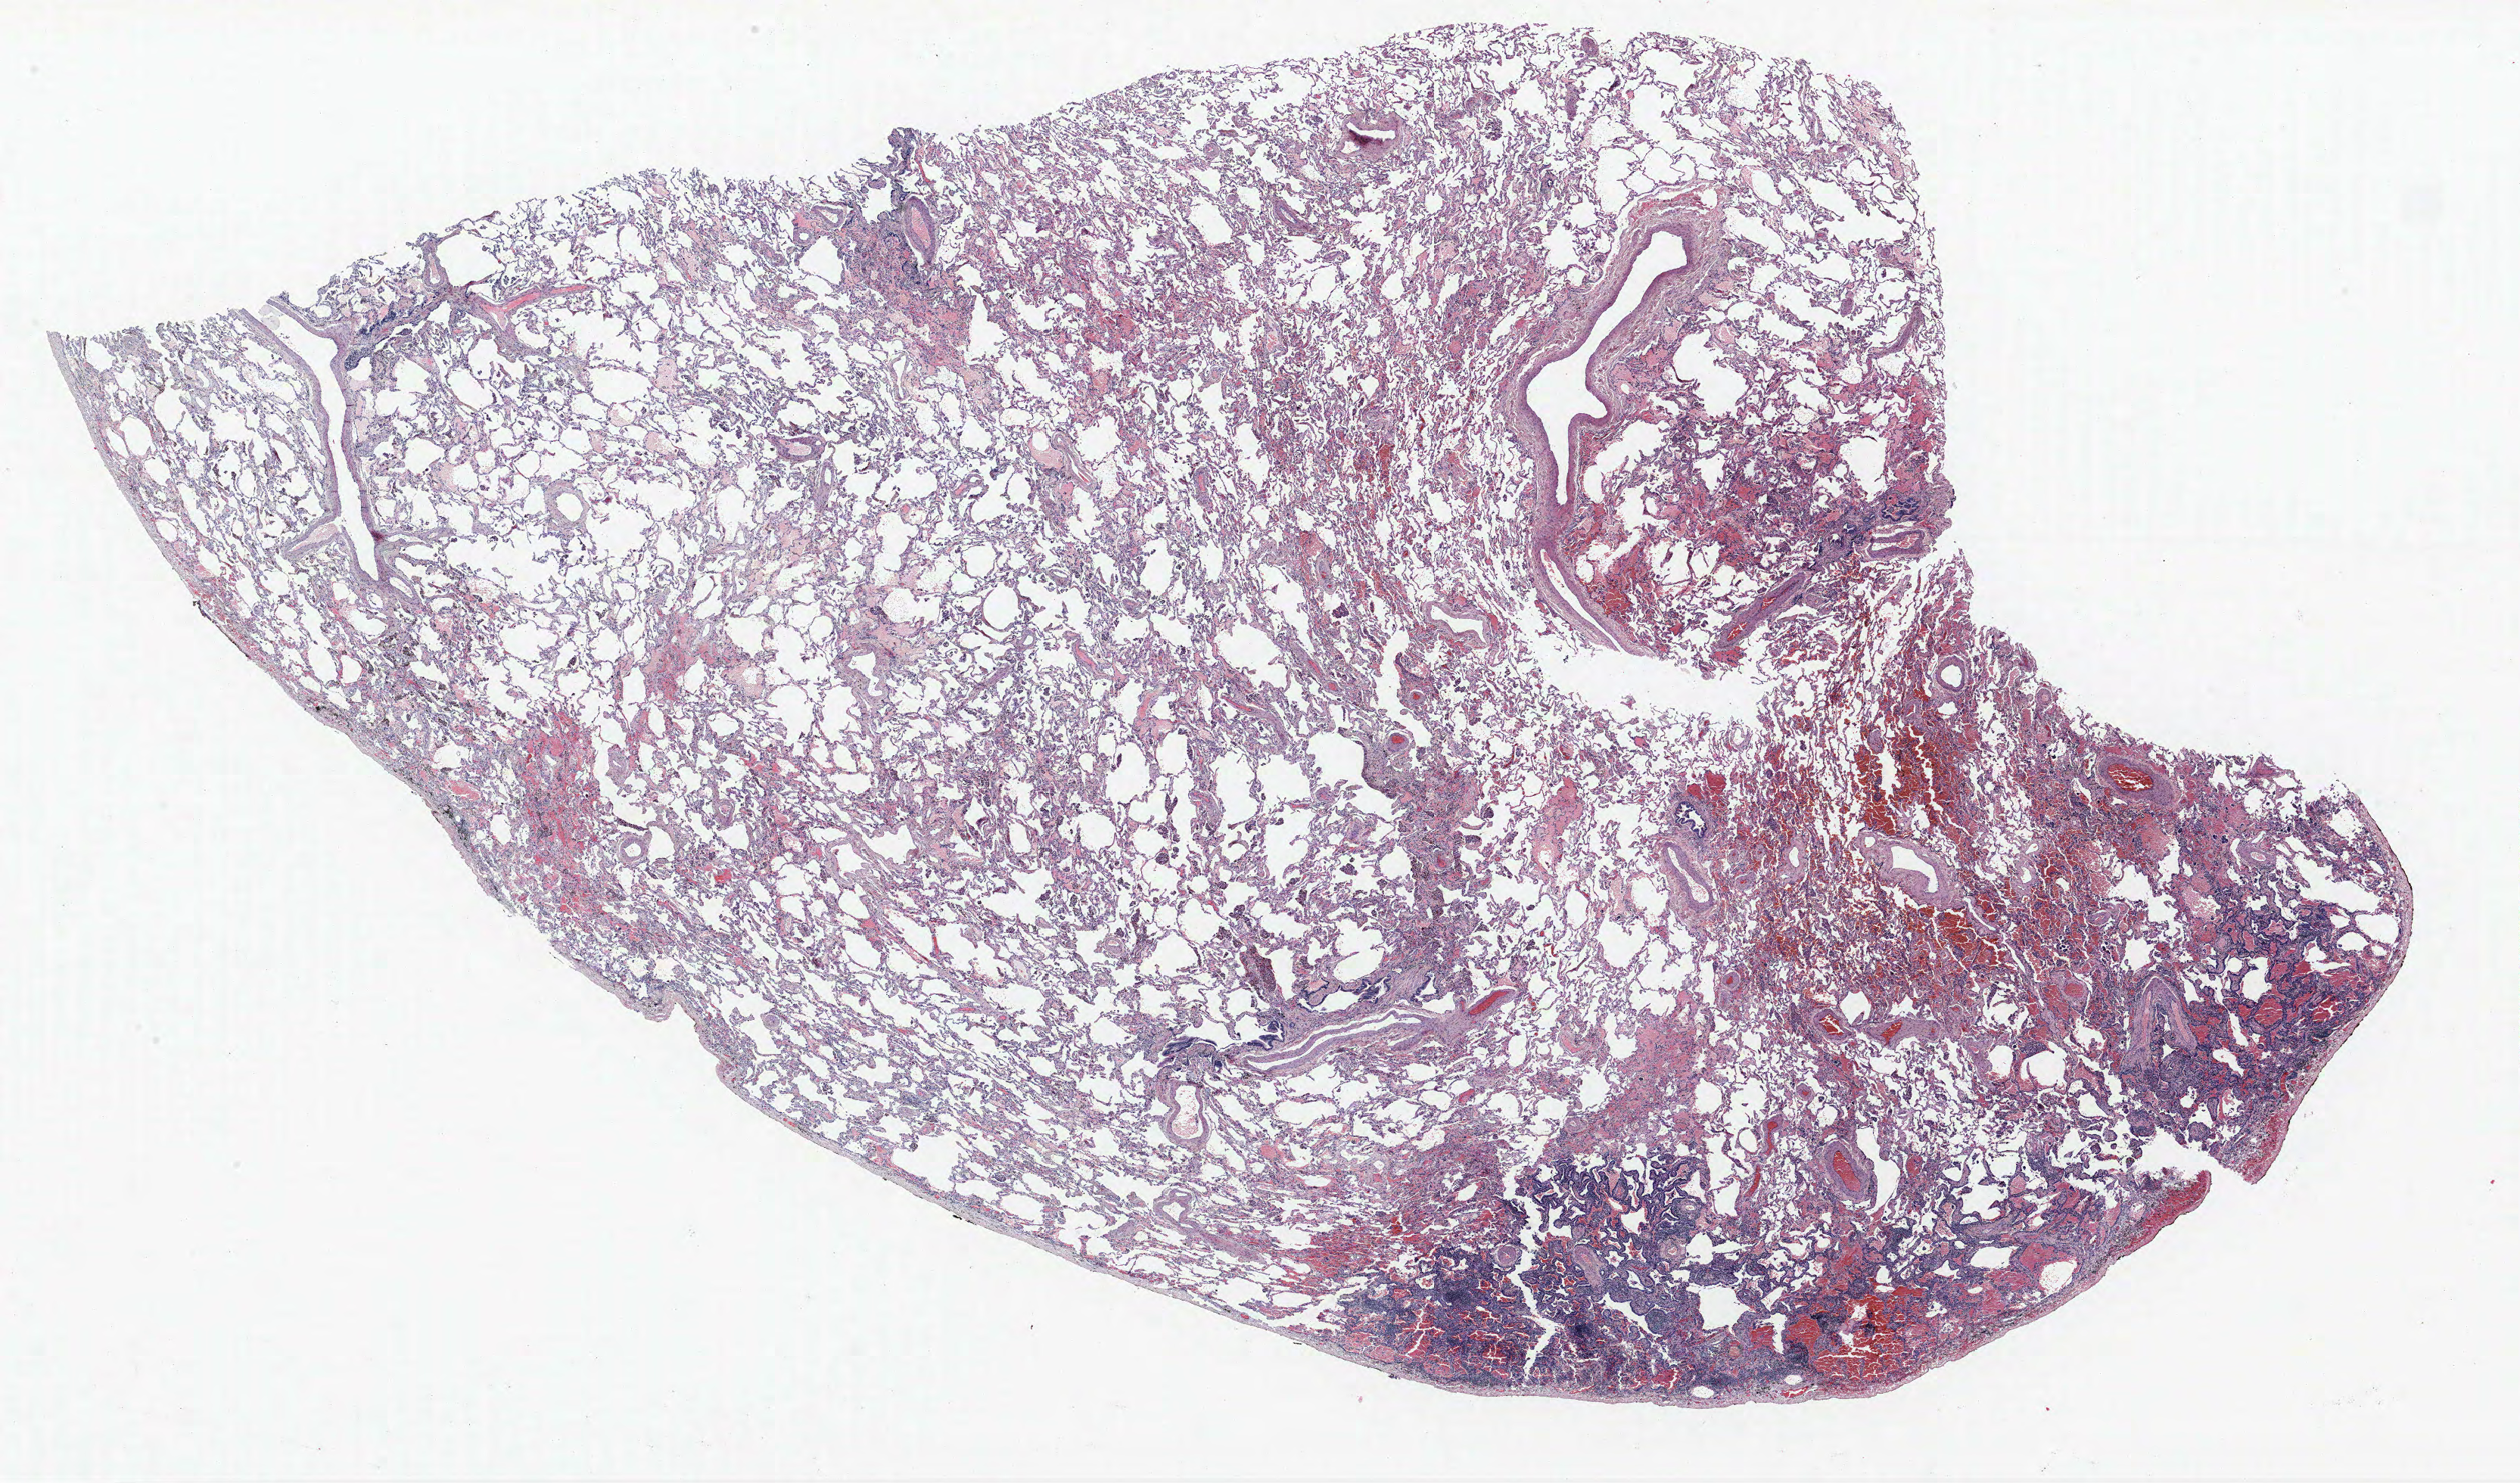
H&E whole-slide image, low-resolution overview of the scanned area, about 26.6 x 15.7 mm (from a 40x scan), formalin-fixed paraffin-embedded (FFPE) section, lung tissue. Male patient, aged 60 at enrolment. Current smoker at enrolment. Grade: well differentiated (G1).
Tumour size (pathology): 27 mm. Participant's lung-cancer diagnosis: Bronchiolo-alveolar adenocarcinoma, NOS (ICD-O-3 8250/3). Stage (AJCC 6th edition): IA. Primary tumour location (clinical record): left upper lobe. ICD-O-3 topography: upper lobe of lung (C34.1).